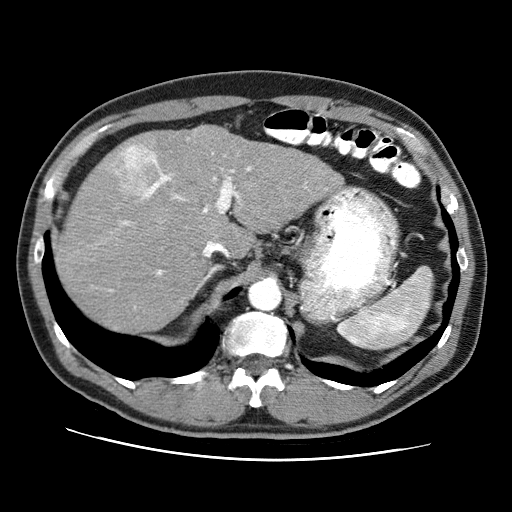
Contrast-enhanced abdominal CT (liver protocol), one axial slice. Slice 51 of 71 in the series (ordered by position). Soft-tissue window (W 400 / L 40 HU). 2.5 mm slice thickness. 512 × 512 image matrix. Case-level facts recorded for this patient, not image findings: diagnosis: hepatocellular carcinoma (patient treated with transarterial chemoembolisation; whether this scan precedes or follows treatment is not stated here); TNM stage (as recorded): Stage-II; Child-Pugh class: A; tumour differentiation: well differentiated; tumour size: 4.6 cm.
Outlined on this slice (semi-automatic segmentation, software-assisted and operator-edited):
- abdominal aorta: bounding box <251,282,279,310> (left, top, right, bottom; pixels)
- liver parenchyma outside the tumour (the mass and vessels are separate outlines, so this box may not span the whole liver): <58,126,342,330>
- mass: <102,143,154,196>
- liver vessels: <124,153,250,274>